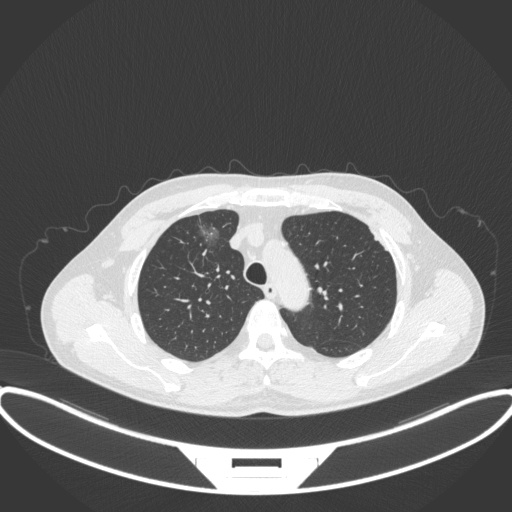
Chest CT, one axial slice. Slice 278 of 395 in the series (ordered by position). Reconstruction kernel B31f. Lung window (W 1500 / L -600 HU). 512 × 512 image matrix, field of view 424 × 424 mm. Male patient, age 60 years. Case-level facts recorded for this patient, not image findings: clinical TNM (as recorded): T1c N0 M0.
Structures marked on this image (bounding box drawn by a radiologist):
- lung tumour (recorded histology: adenocarcinoma): box from (x=190, y=213) to (x=224, y=256) px